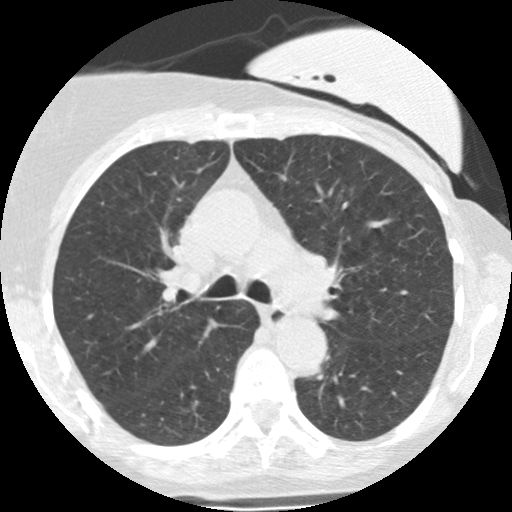
Axial slice from a low-dose chest CT screening exam; second annual screen; lung window (W 1500 / L -600 HU); 2.5 mm slice thickness; standard (soft-tissue) reconstruction kernel (STANDARD); slice 90 of 251 in the series. Female participant, aged 66 years at enrolment. Former smoker at enrolment.
Expert reader's lesion annotation, box from (x=344, y=181) to (x=359, y=201) px. The exam's reader record, not a measurement of the box and not confirmed to be the same lesion: non-calcified nodule or mass ≥4 mm, left upper lobe, 7 × 5 mm, smooth margins, soft tissue attenuation, pre-existing on the prior screen: yes; interval growth: yes.